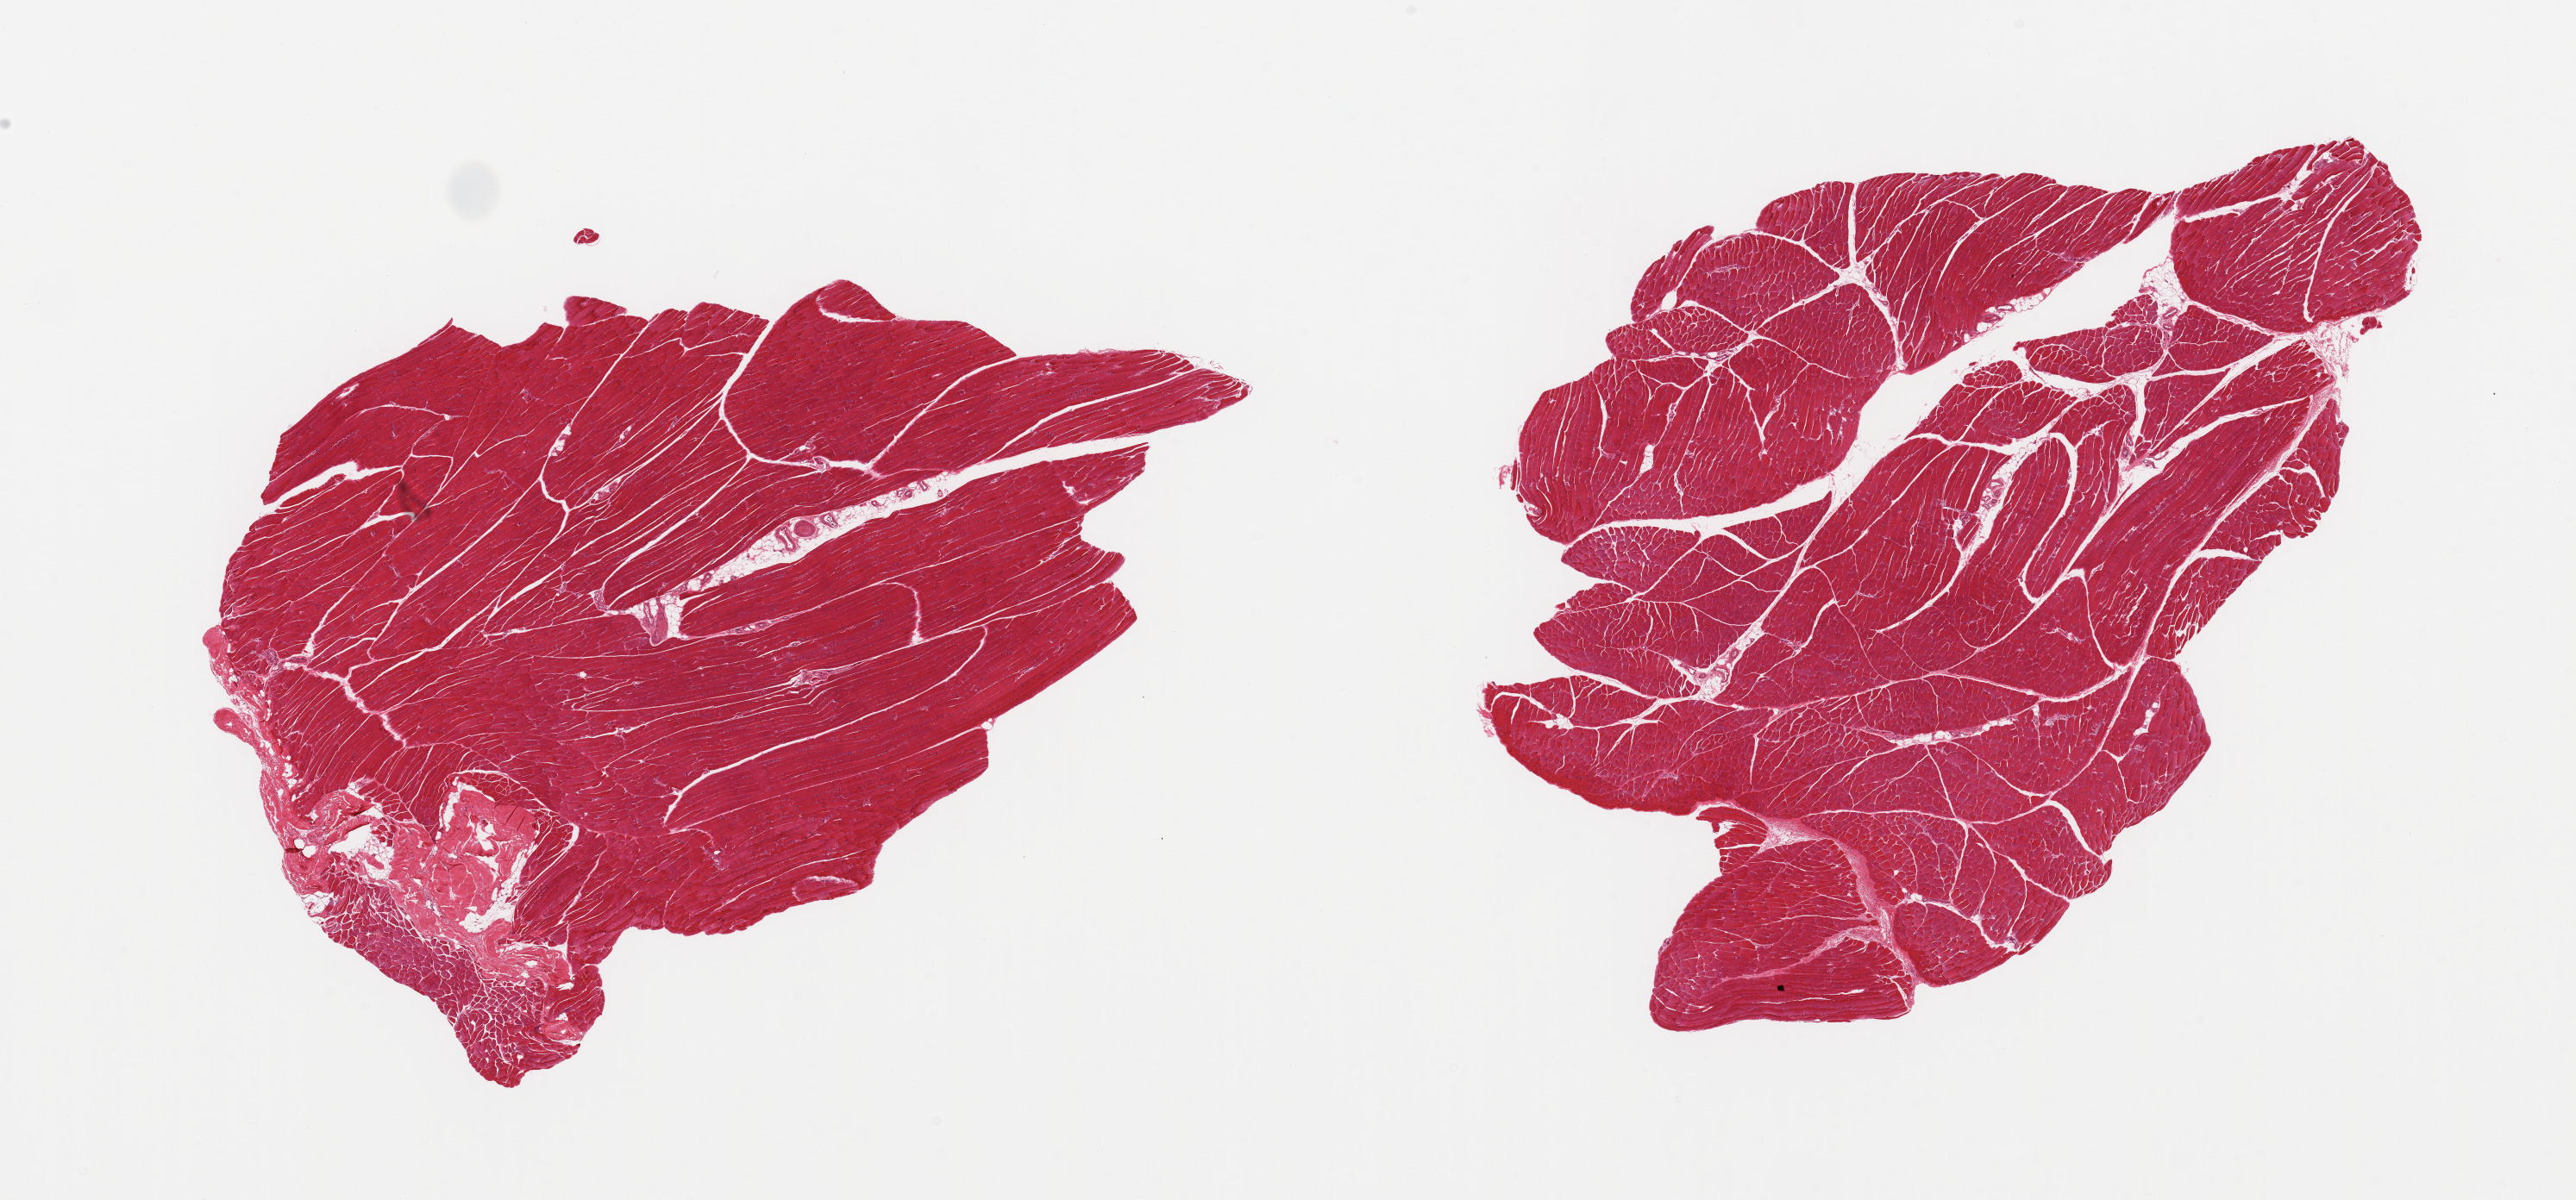
Whole-slide image, haematoxylin and eosin stain, brightfield, whole scanned area (about 23.6 x 11.0 mm) shown as a low-resolution overview; PAXgene-fixed paraffin-embedded (PFPE) section; target tissue: skeletal muscle; donor tissue sample. Donor: female.
Pathologist's review note for this sample: 2 pieces, focal tendon/; ~5-10% interstitial fat.